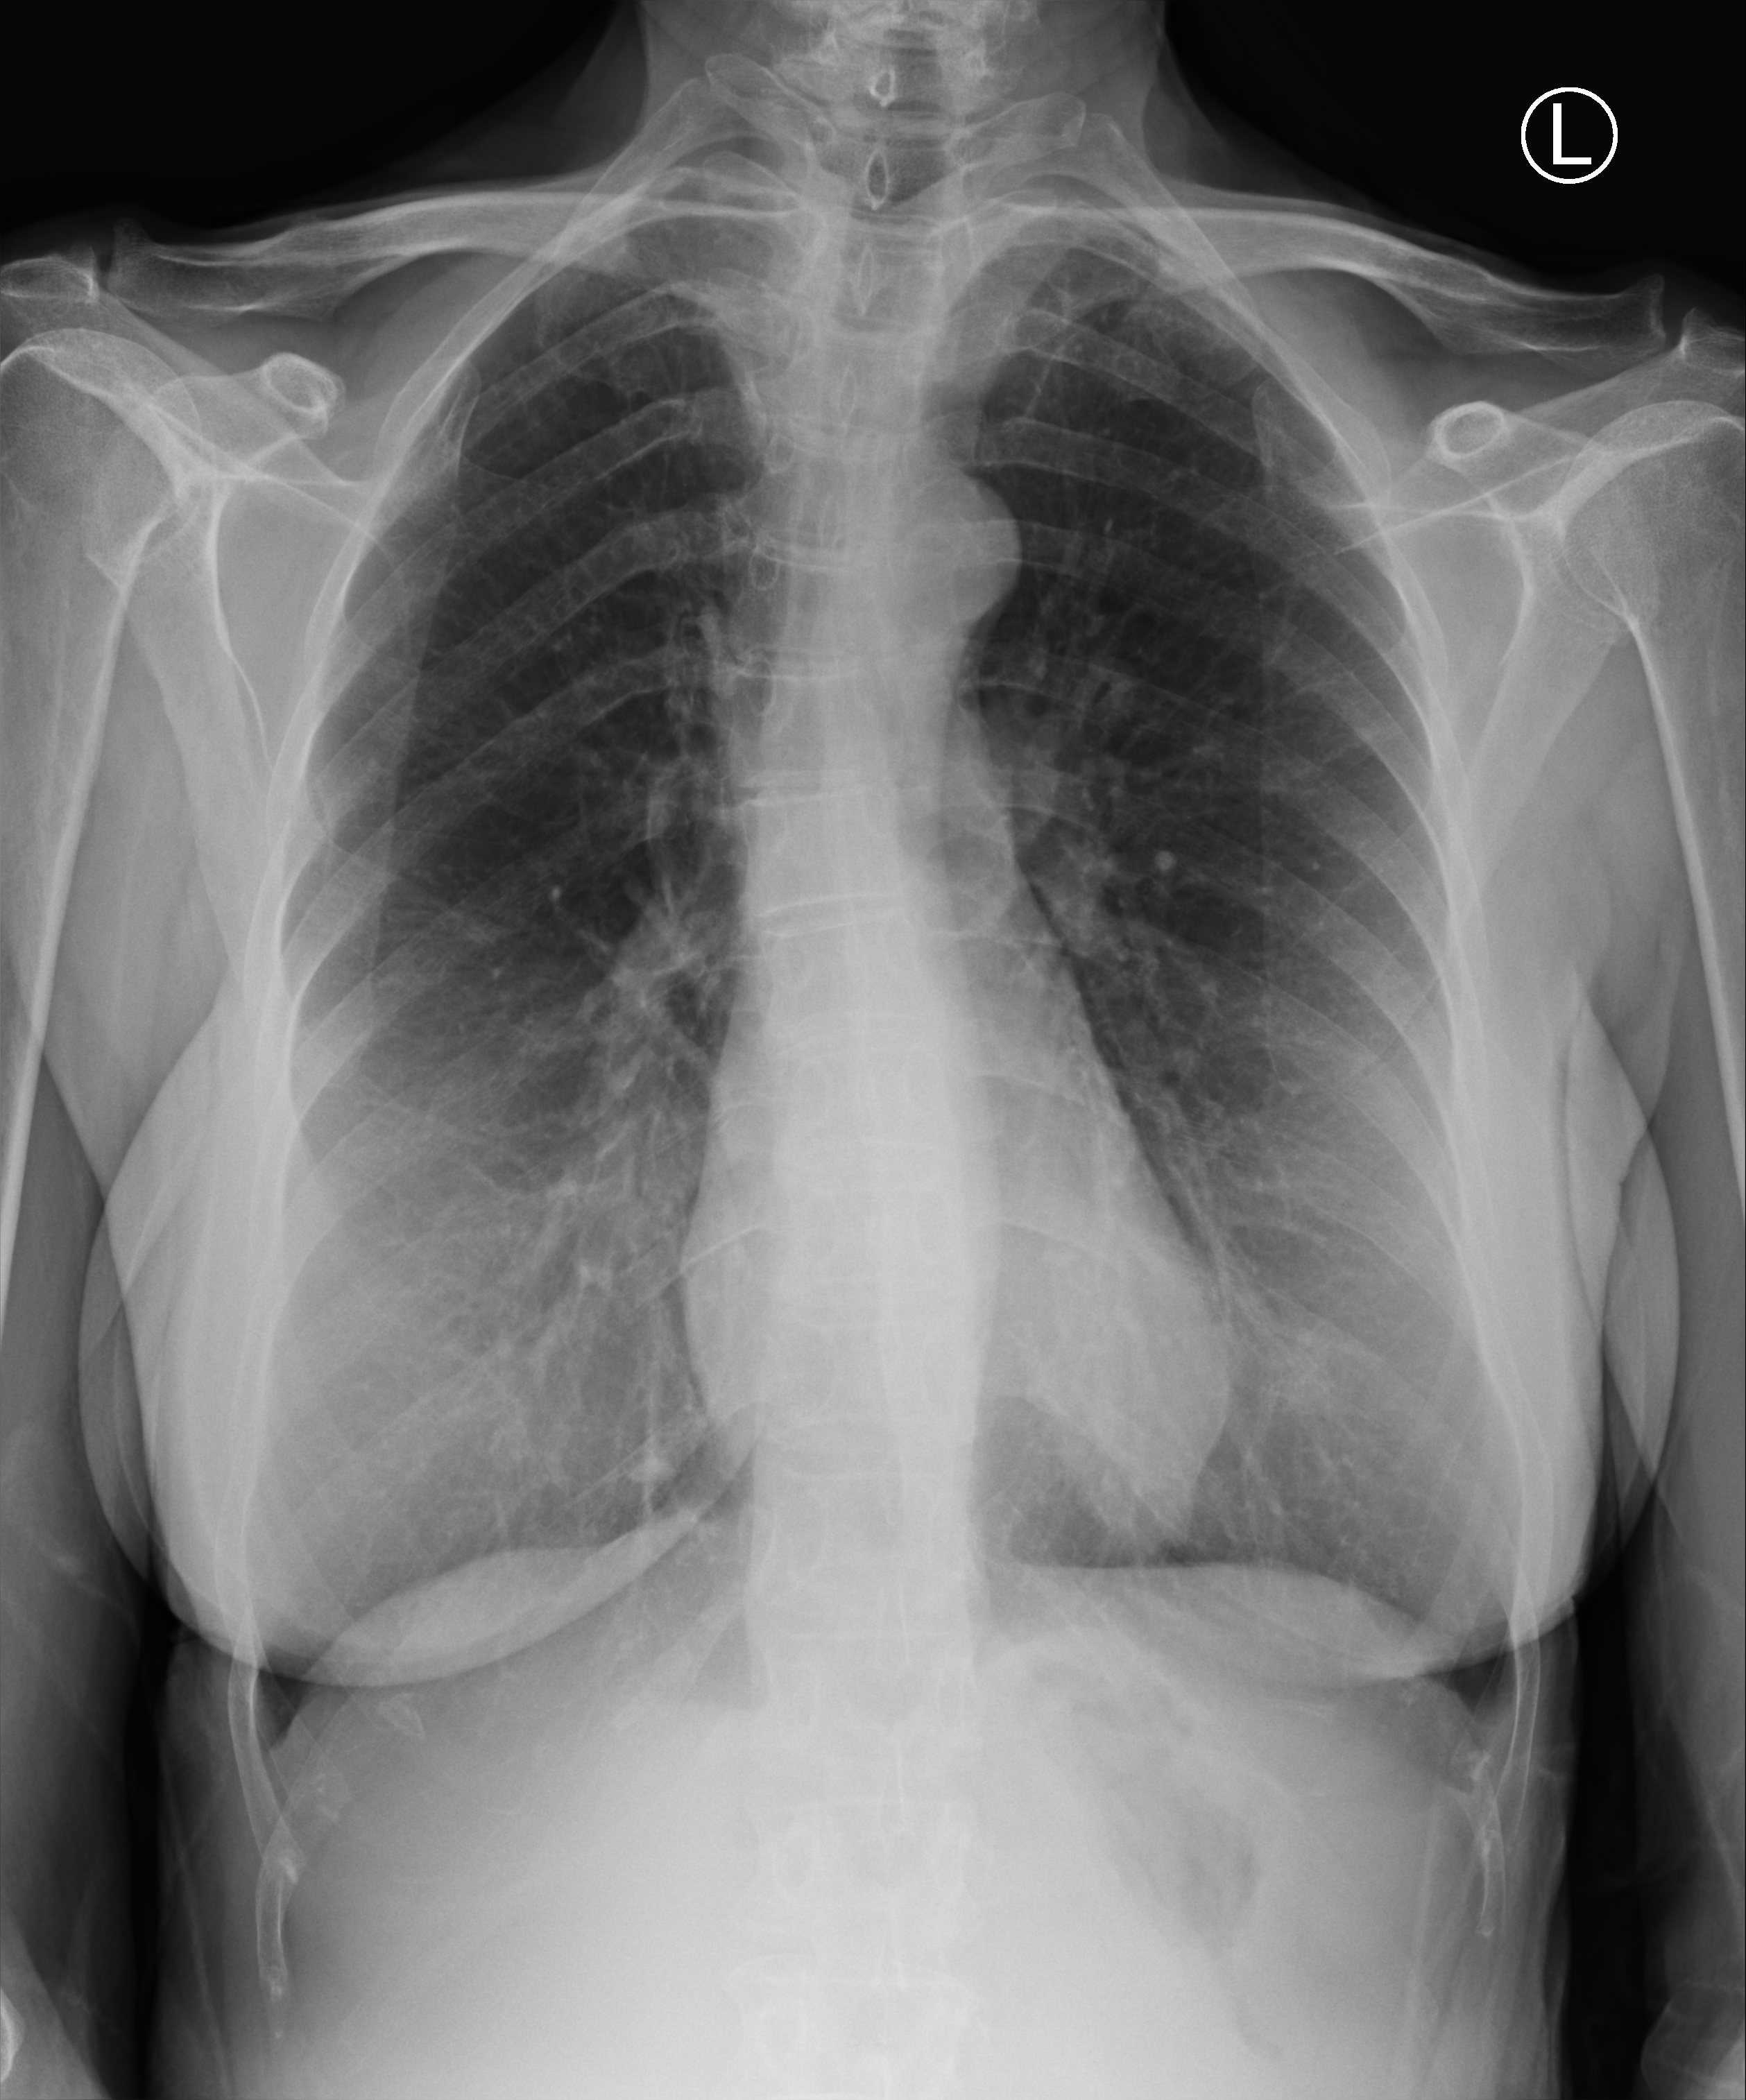
Chest X-ray (portable); anteroposterior (AP) projection. Patient hospitalised with COVID-19; female, aged 60–74 years.
Hospital-stay facts (about this admission, not read from this image; timing relative to this image not recorded): chronic kidney disease (admission record): no.